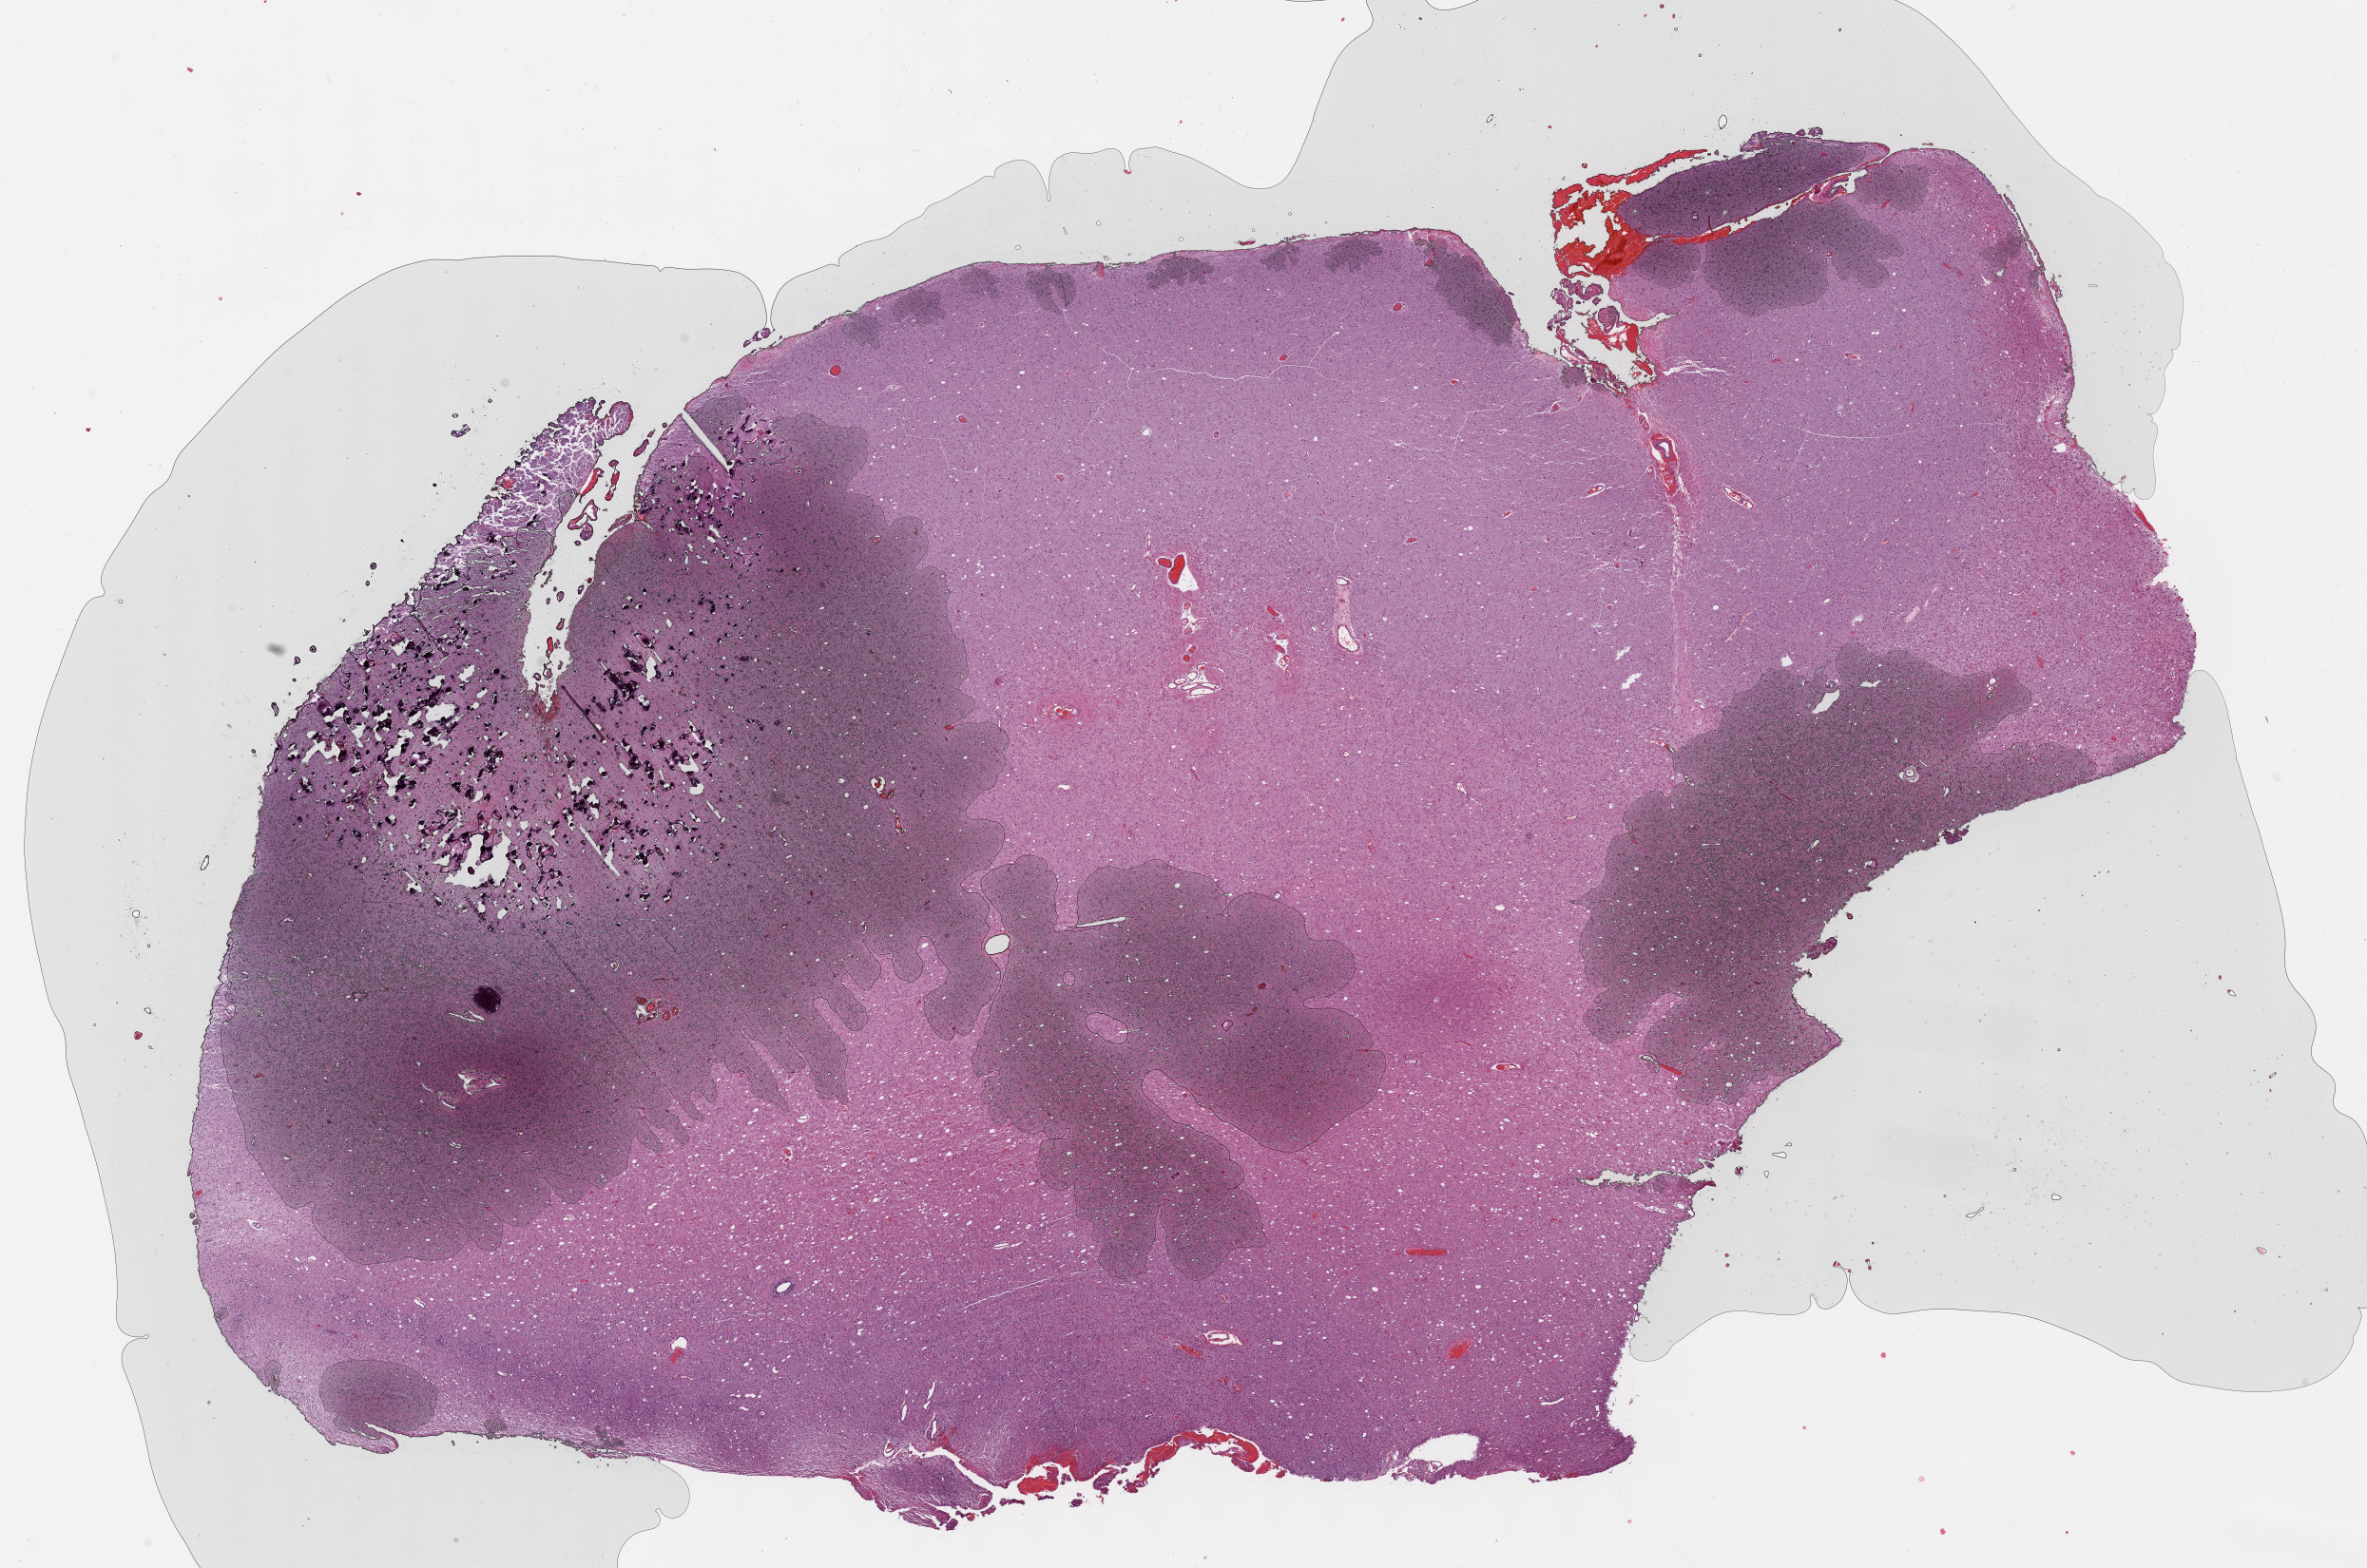
Whole-slide histology image, H&E — low-resolution overview of the scanned area, about 20.1 x 13.3 mm (acquisition: 40x scan). Formalin-fixed paraffin-embedded (FFPE) diagnostic section. Primary tumour sample from the brain. Male, age 58 years at initial diagnosis. Histologic grade: G3 (poorly differentiated).
Pathologic diagnosis: Mixed glioma (cerebrum).